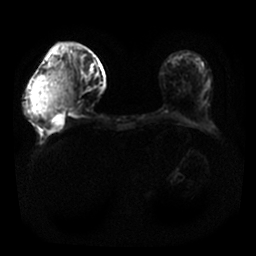
Breast MRI, one axial slice. Position 1 of 25 along the scan axis. Diffusion-weighted series; image 2 of 4 stored at this slice position (different b-values; order by instance number). 1.5 T. 4 mm slice thickness. 256 × 256 image matrix, field of view 340 × 340 mm. Female patient.
Structures marked on this image (manually delineated by an expert):
- tumour on diffusion-weighted imaging: bounding box (x1, y1, x2, y2) in pixels: (33, 71, 74, 118)